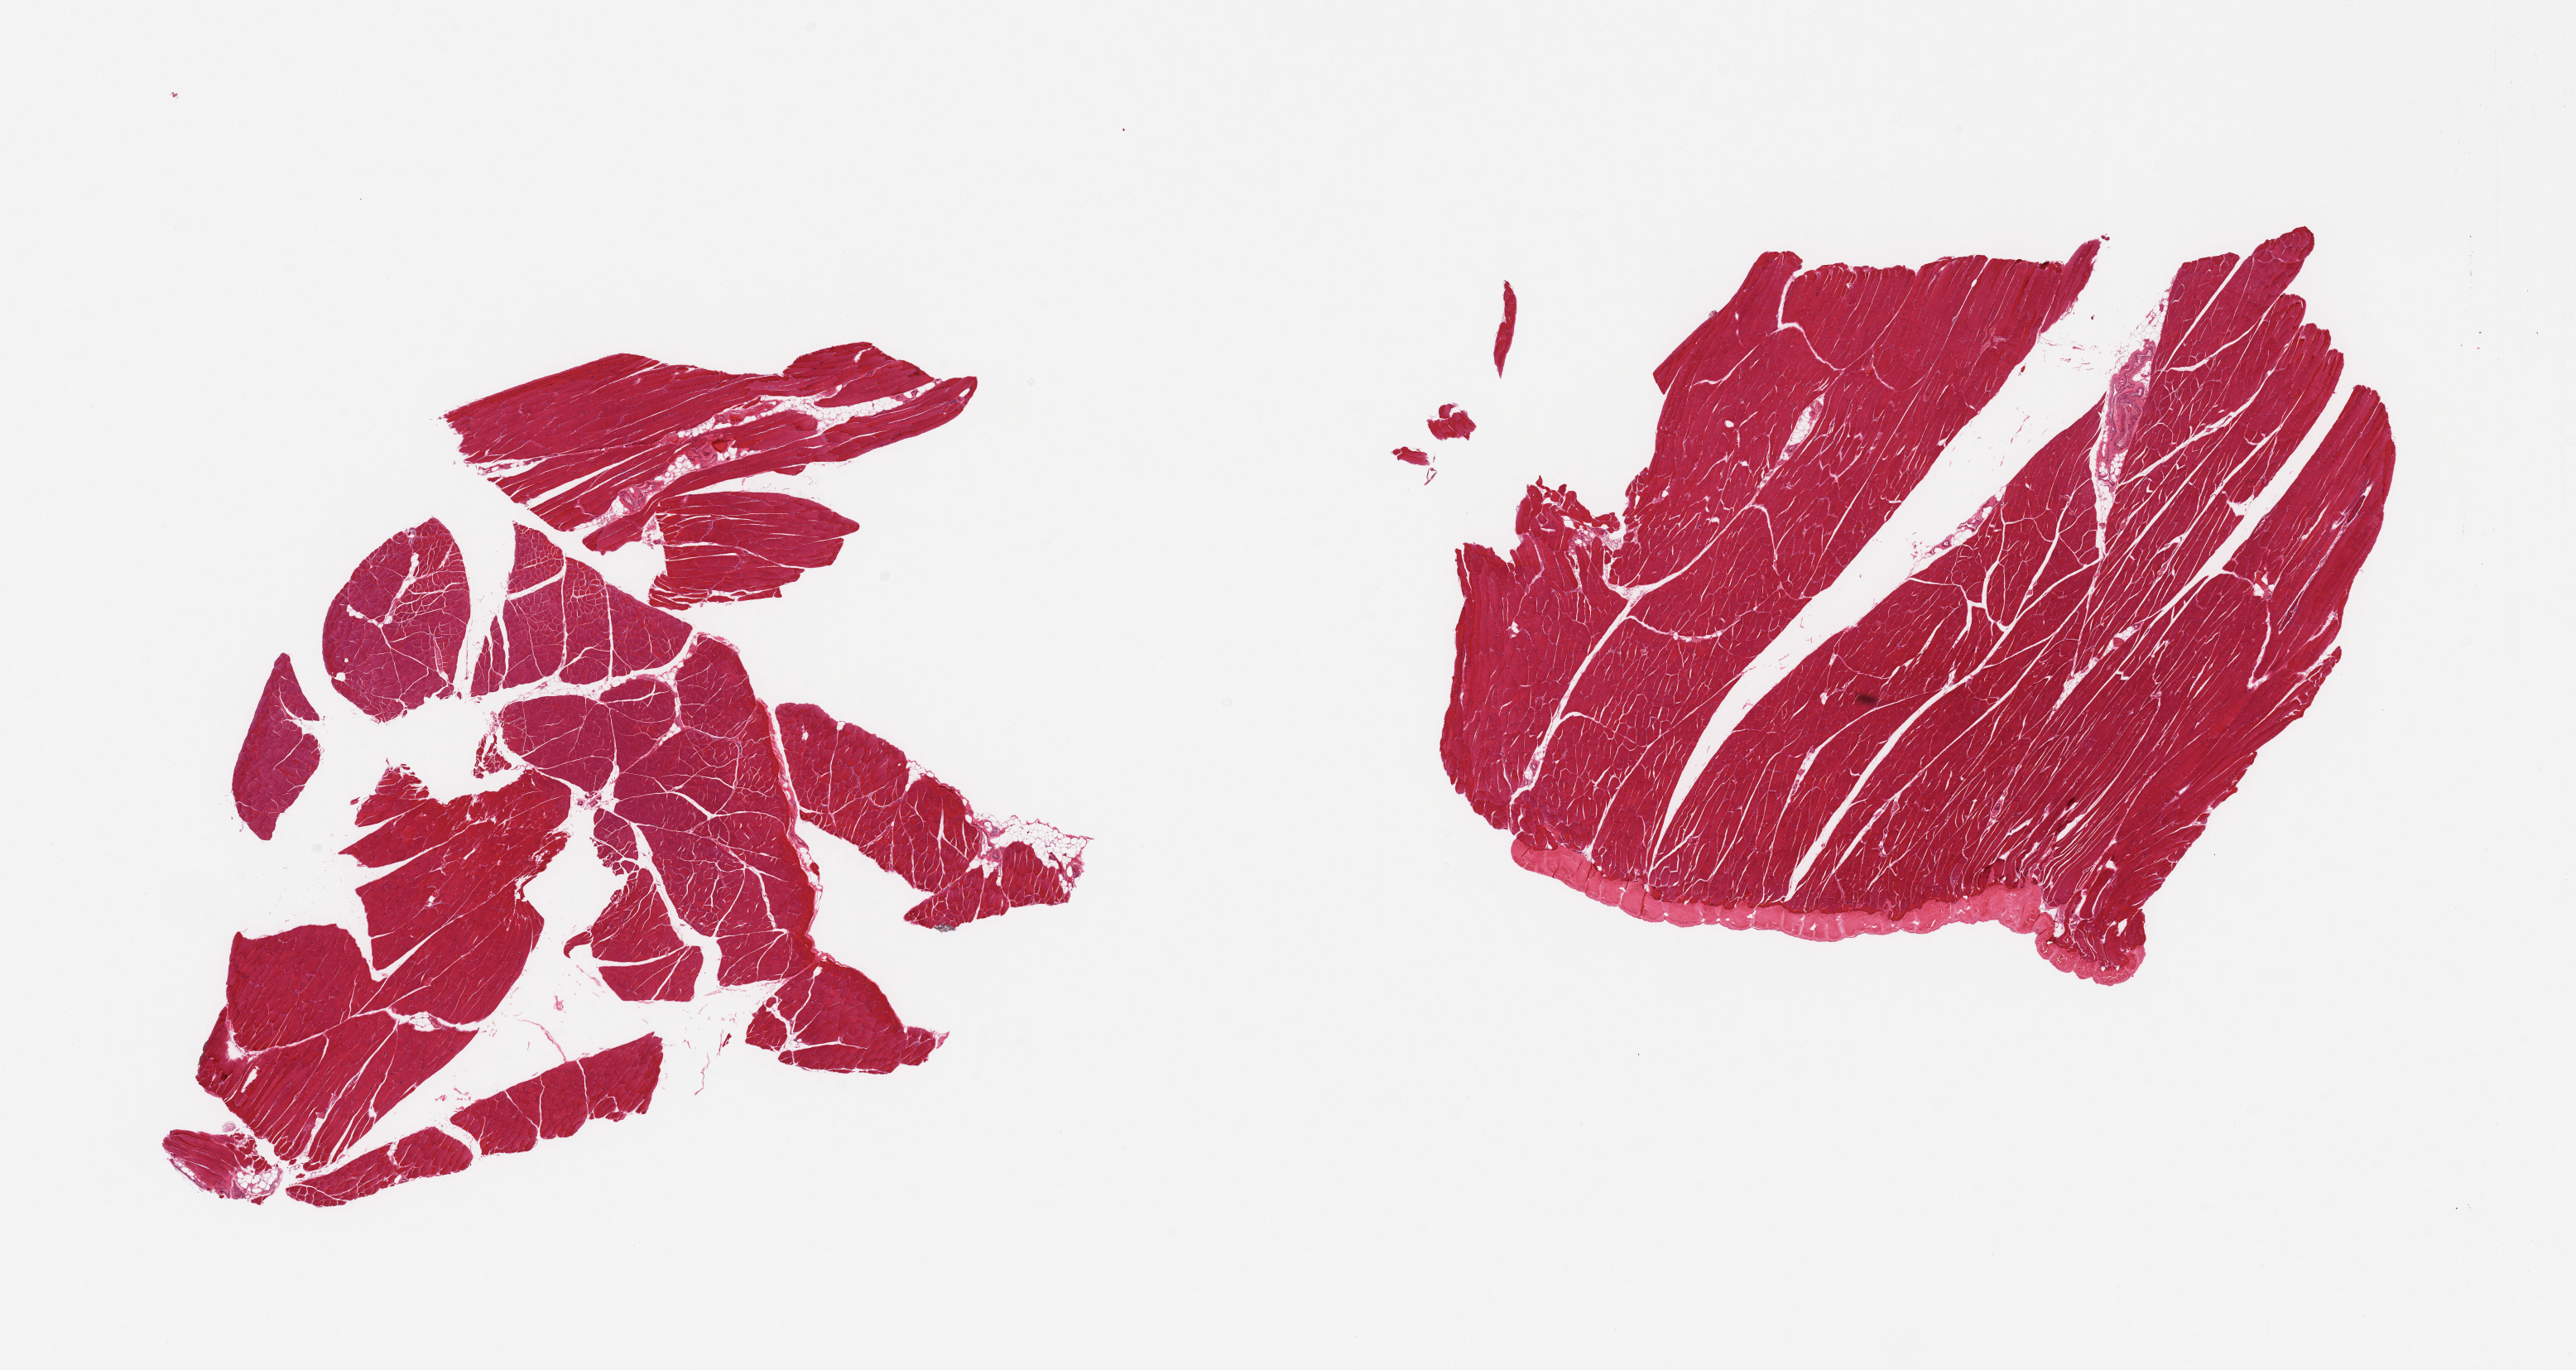
Whole-slide image, hematoxylin and eosin (H&E) stain — a low-resolution overview of the entire scanned area, about 24.6 x 13.1 mm, PAXgene-fixed, paraffin-embedded tissue, section of skeletal muscle (target tissue), tissue donor sample. Male donor.
- reviewer comment on this tissue sample: 2 pieces